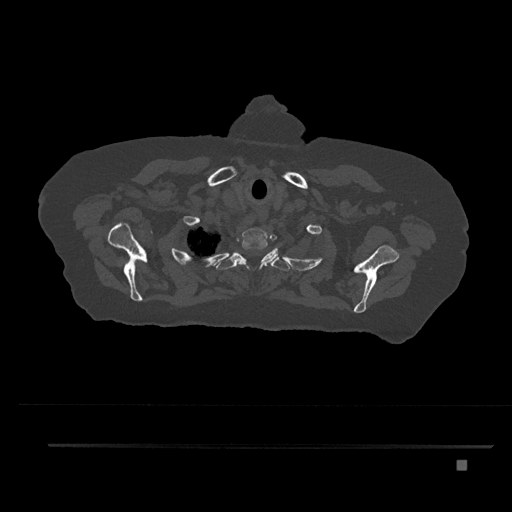
CT including the spine, one axial slice; slice 683 of 797 in the series (ordered by position); reconstruction kernel Br40s/3; bone window (W 1800 / L 400 HU); 512 × 512 image matrix, field of view 437 × 437 mm. Patient: female, 76 years. Case-level facts recorded for this patient, not image findings: primary cancer: lung; vertebrae with lytic lesions (as recorded): T11, L3.
Annotated regions visible in this slice (semi-automatic segmentation, software-assisted and operator-edited):
- T1 vertebra: bounding box (x1, y1, x2, y2) in pixels: (237, 228, 278, 270)
- T2 vertebra: (216, 248, 290, 271)